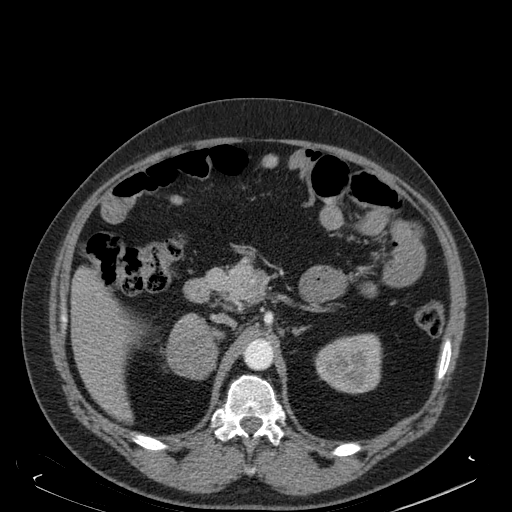
Contrast-enhanced abdominal CT, one axial slice; position 108 of 181 along the scan axis; soft-tissue window (W 400 / L 40 HU); 512 × 512 image matrix, field of view 405 × 405 mm. Male patient. From the clinical record (not read from this slice): diagnosis: adrenocortical carcinoma; tumour side: right adrenal; tumour size at pathology: 7.5 cm; Ki-67 index: 25 %; stage (as recorded): 4.
Structures marked on this image (semi-automatically segmented with operator editing):
- mass: bounding box [x1, y1, x2, y2] px = [168, 313, 216, 377]